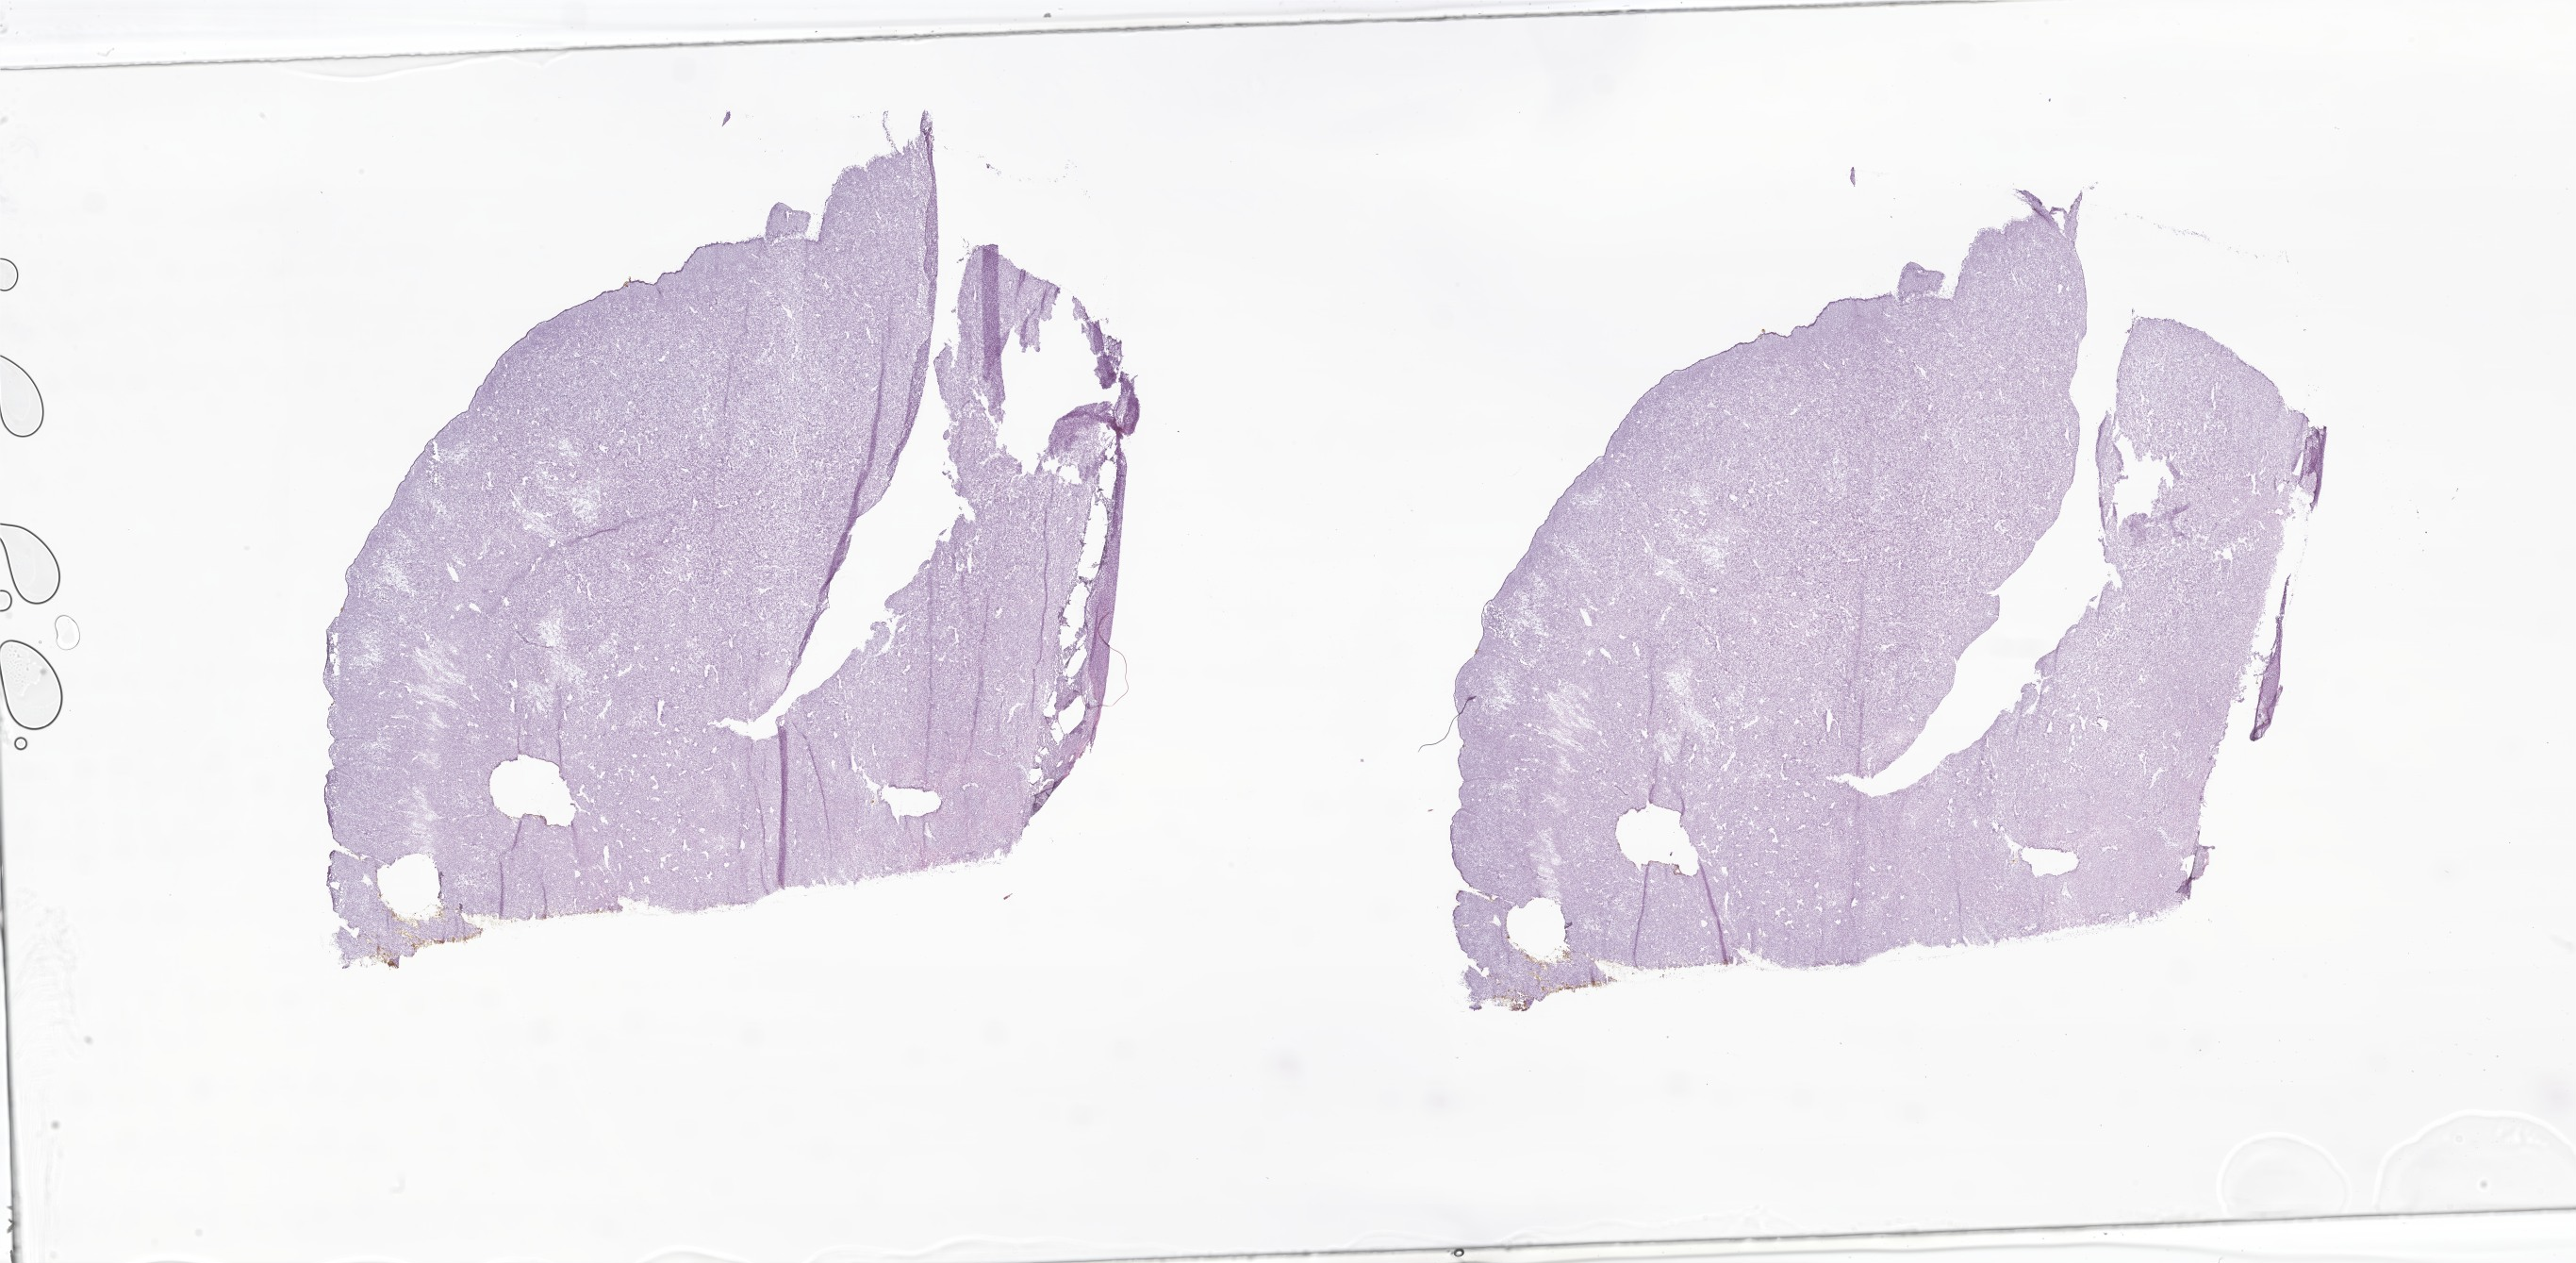
Digitized H&E-stained section of tumor tissue from the soft tissue of abdomen, whole scanned area (about 46.1 x 22.6 mm) shown as a low-resolution overview. Frozen section. Male patient, age 169 months (14 years 1 month).
Recorded diagnosis: Synovial sarcoma, NOS.